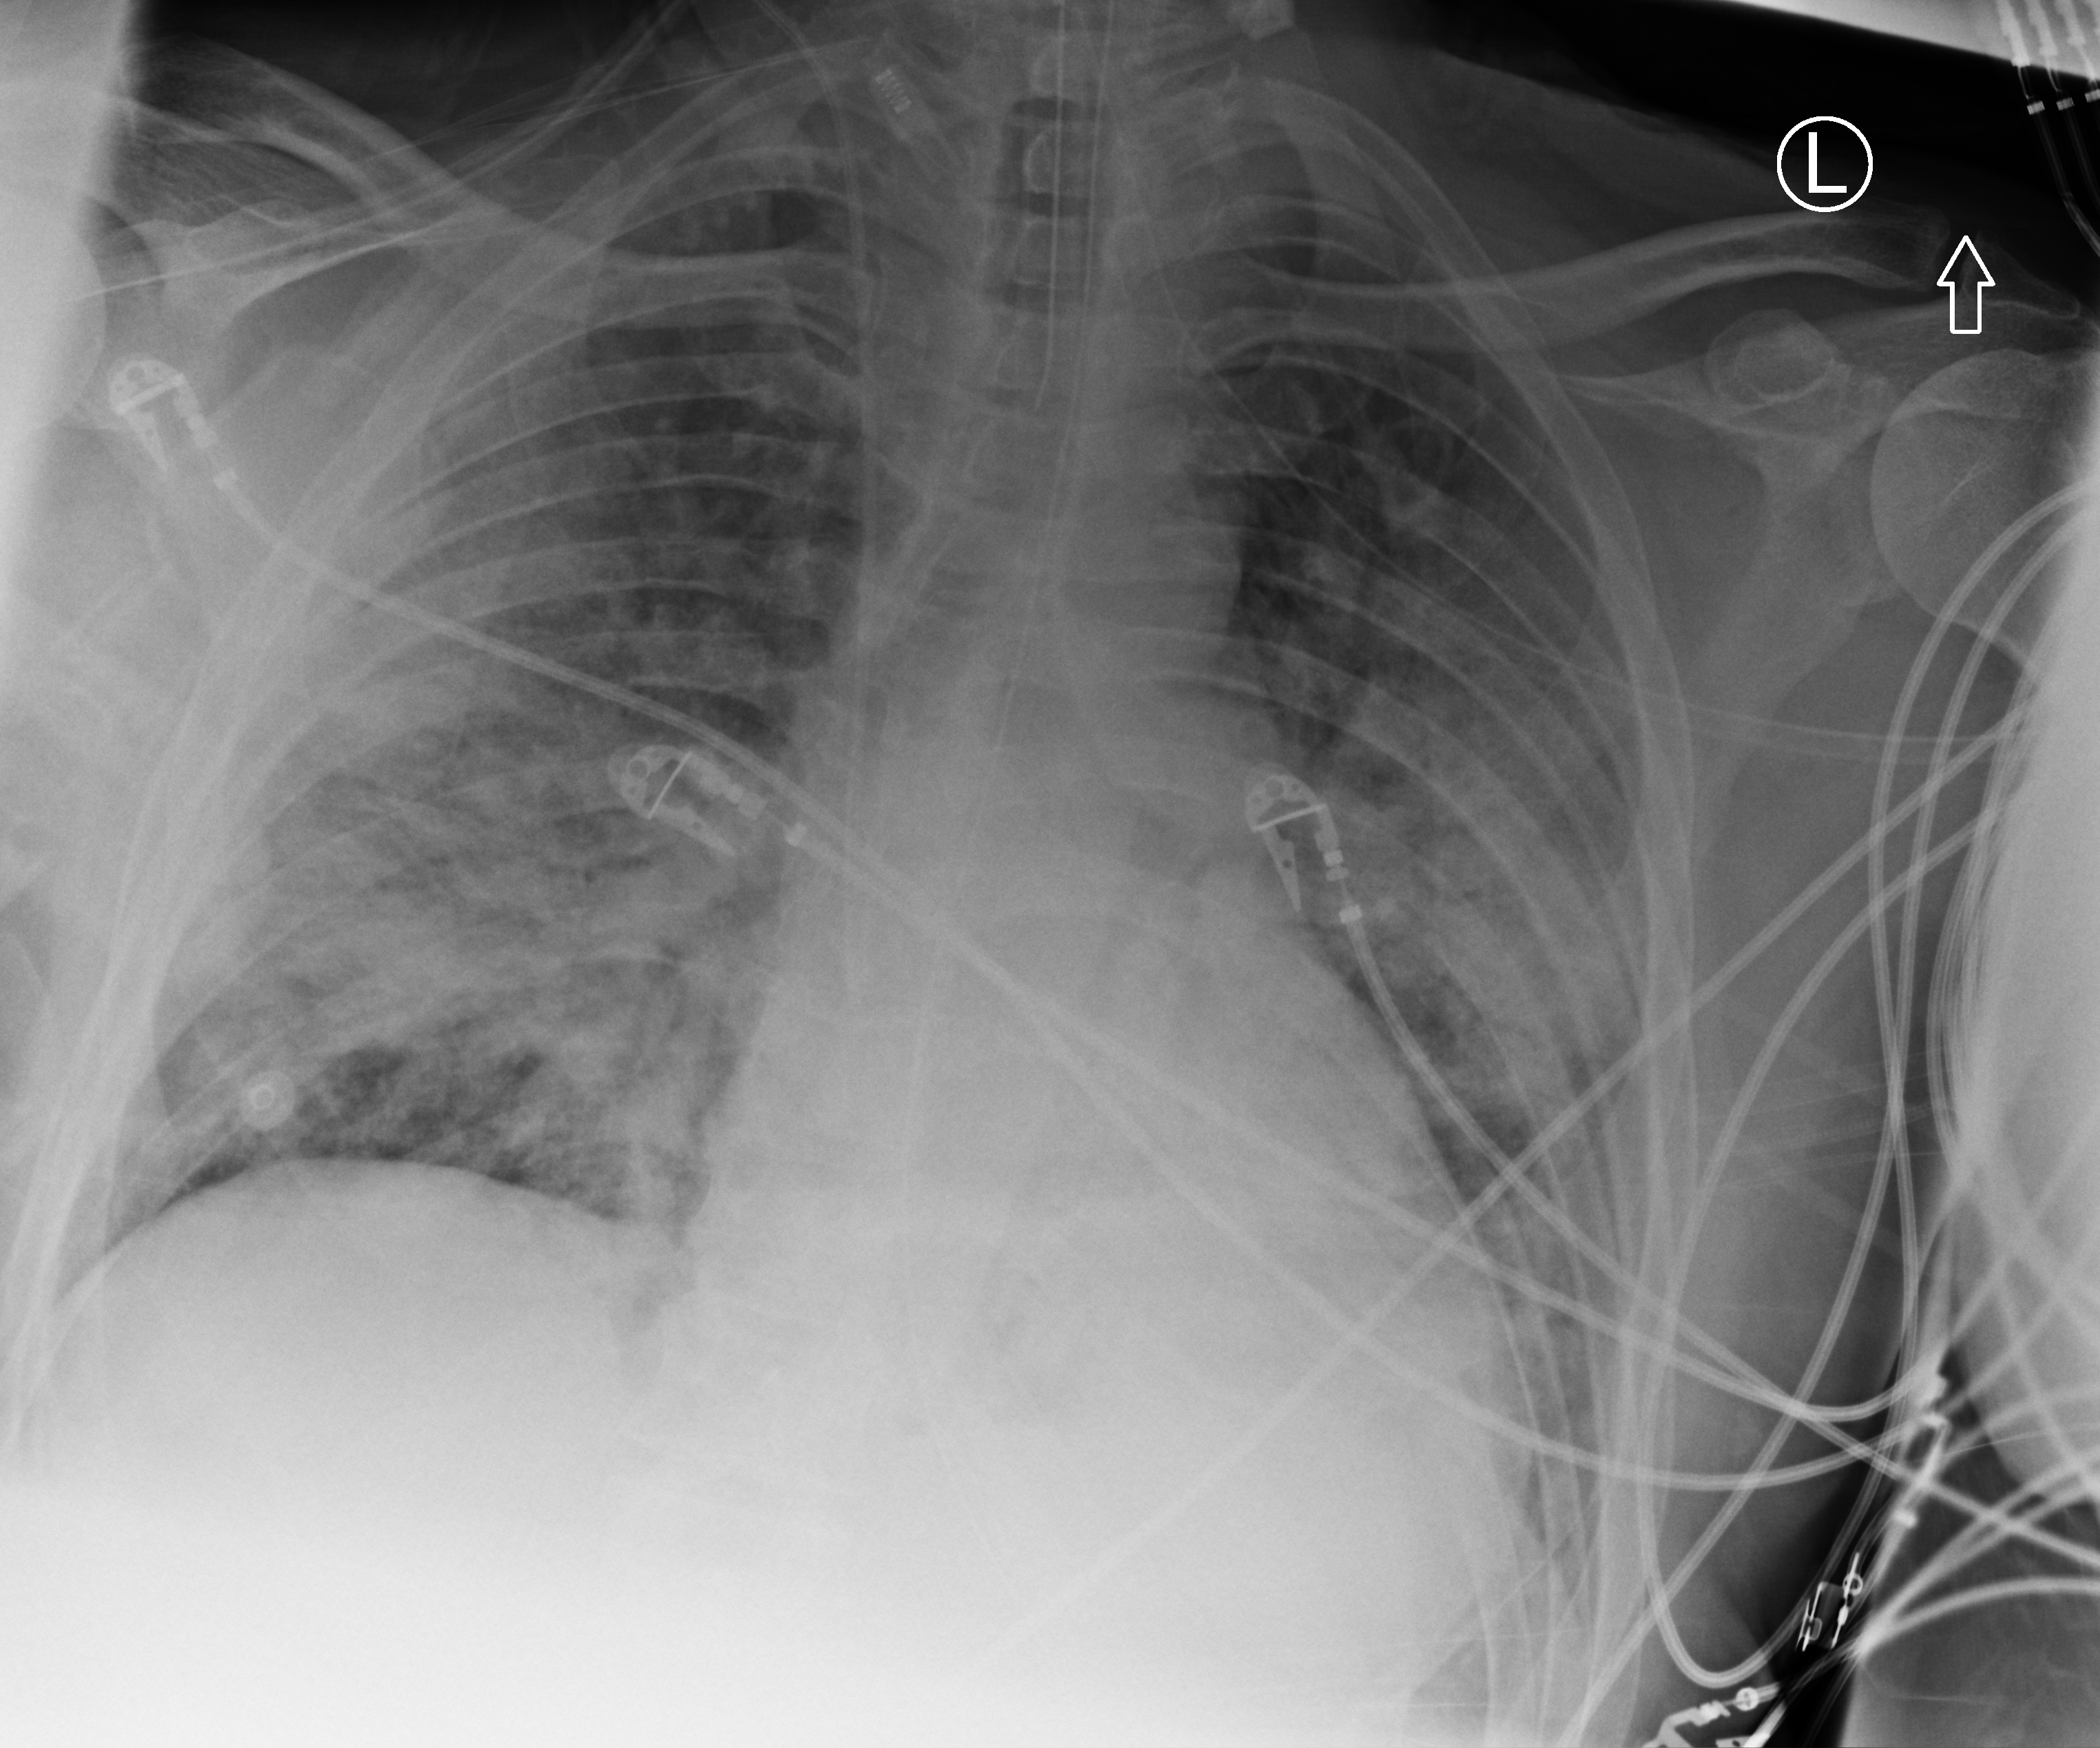
Portable chest radiograph, anteroposterior (AP) projection. Patient hospitalised with COVID-19; male, aged 18–59 years.
From the hospital-stay record, not from the radiograph (when in the stay this image was taken is not recorded):
- diabetes (admission record): no
- mechanically ventilated during this hospital stay: yes